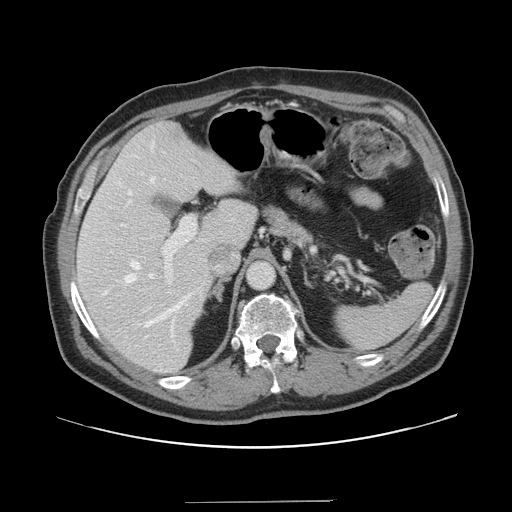
Contrast-enhanced abdominal CT, one axial slice. Slice 99 of 151 in the series (ordered by position). 120 kVp. Soft-tissue window (W 400 / L 40 HU). 2.5 mm slice thickness. 512 × 512 image matrix, field of view 399 × 399 mm. Male patient, age 63 years. From the clinical record (not read from this slice): diagnosis: colorectal cancer liver metastases, imaged before liver resection; multiple liver metastases: no; largest metastasis: 2.1 cm; disease in both lobes: no.
Outlined on this slice (expert manual segmentation):
- hepatic veins: bounding box <104,144,200,343> (left, top, right, bottom; pixels)
- liver: <78,122,257,372>
- planned liver remnant (the part of the liver to remain after resection): <78,122,255,373>
- portal vein (with intrahepatic branches): <144,216,196,312>